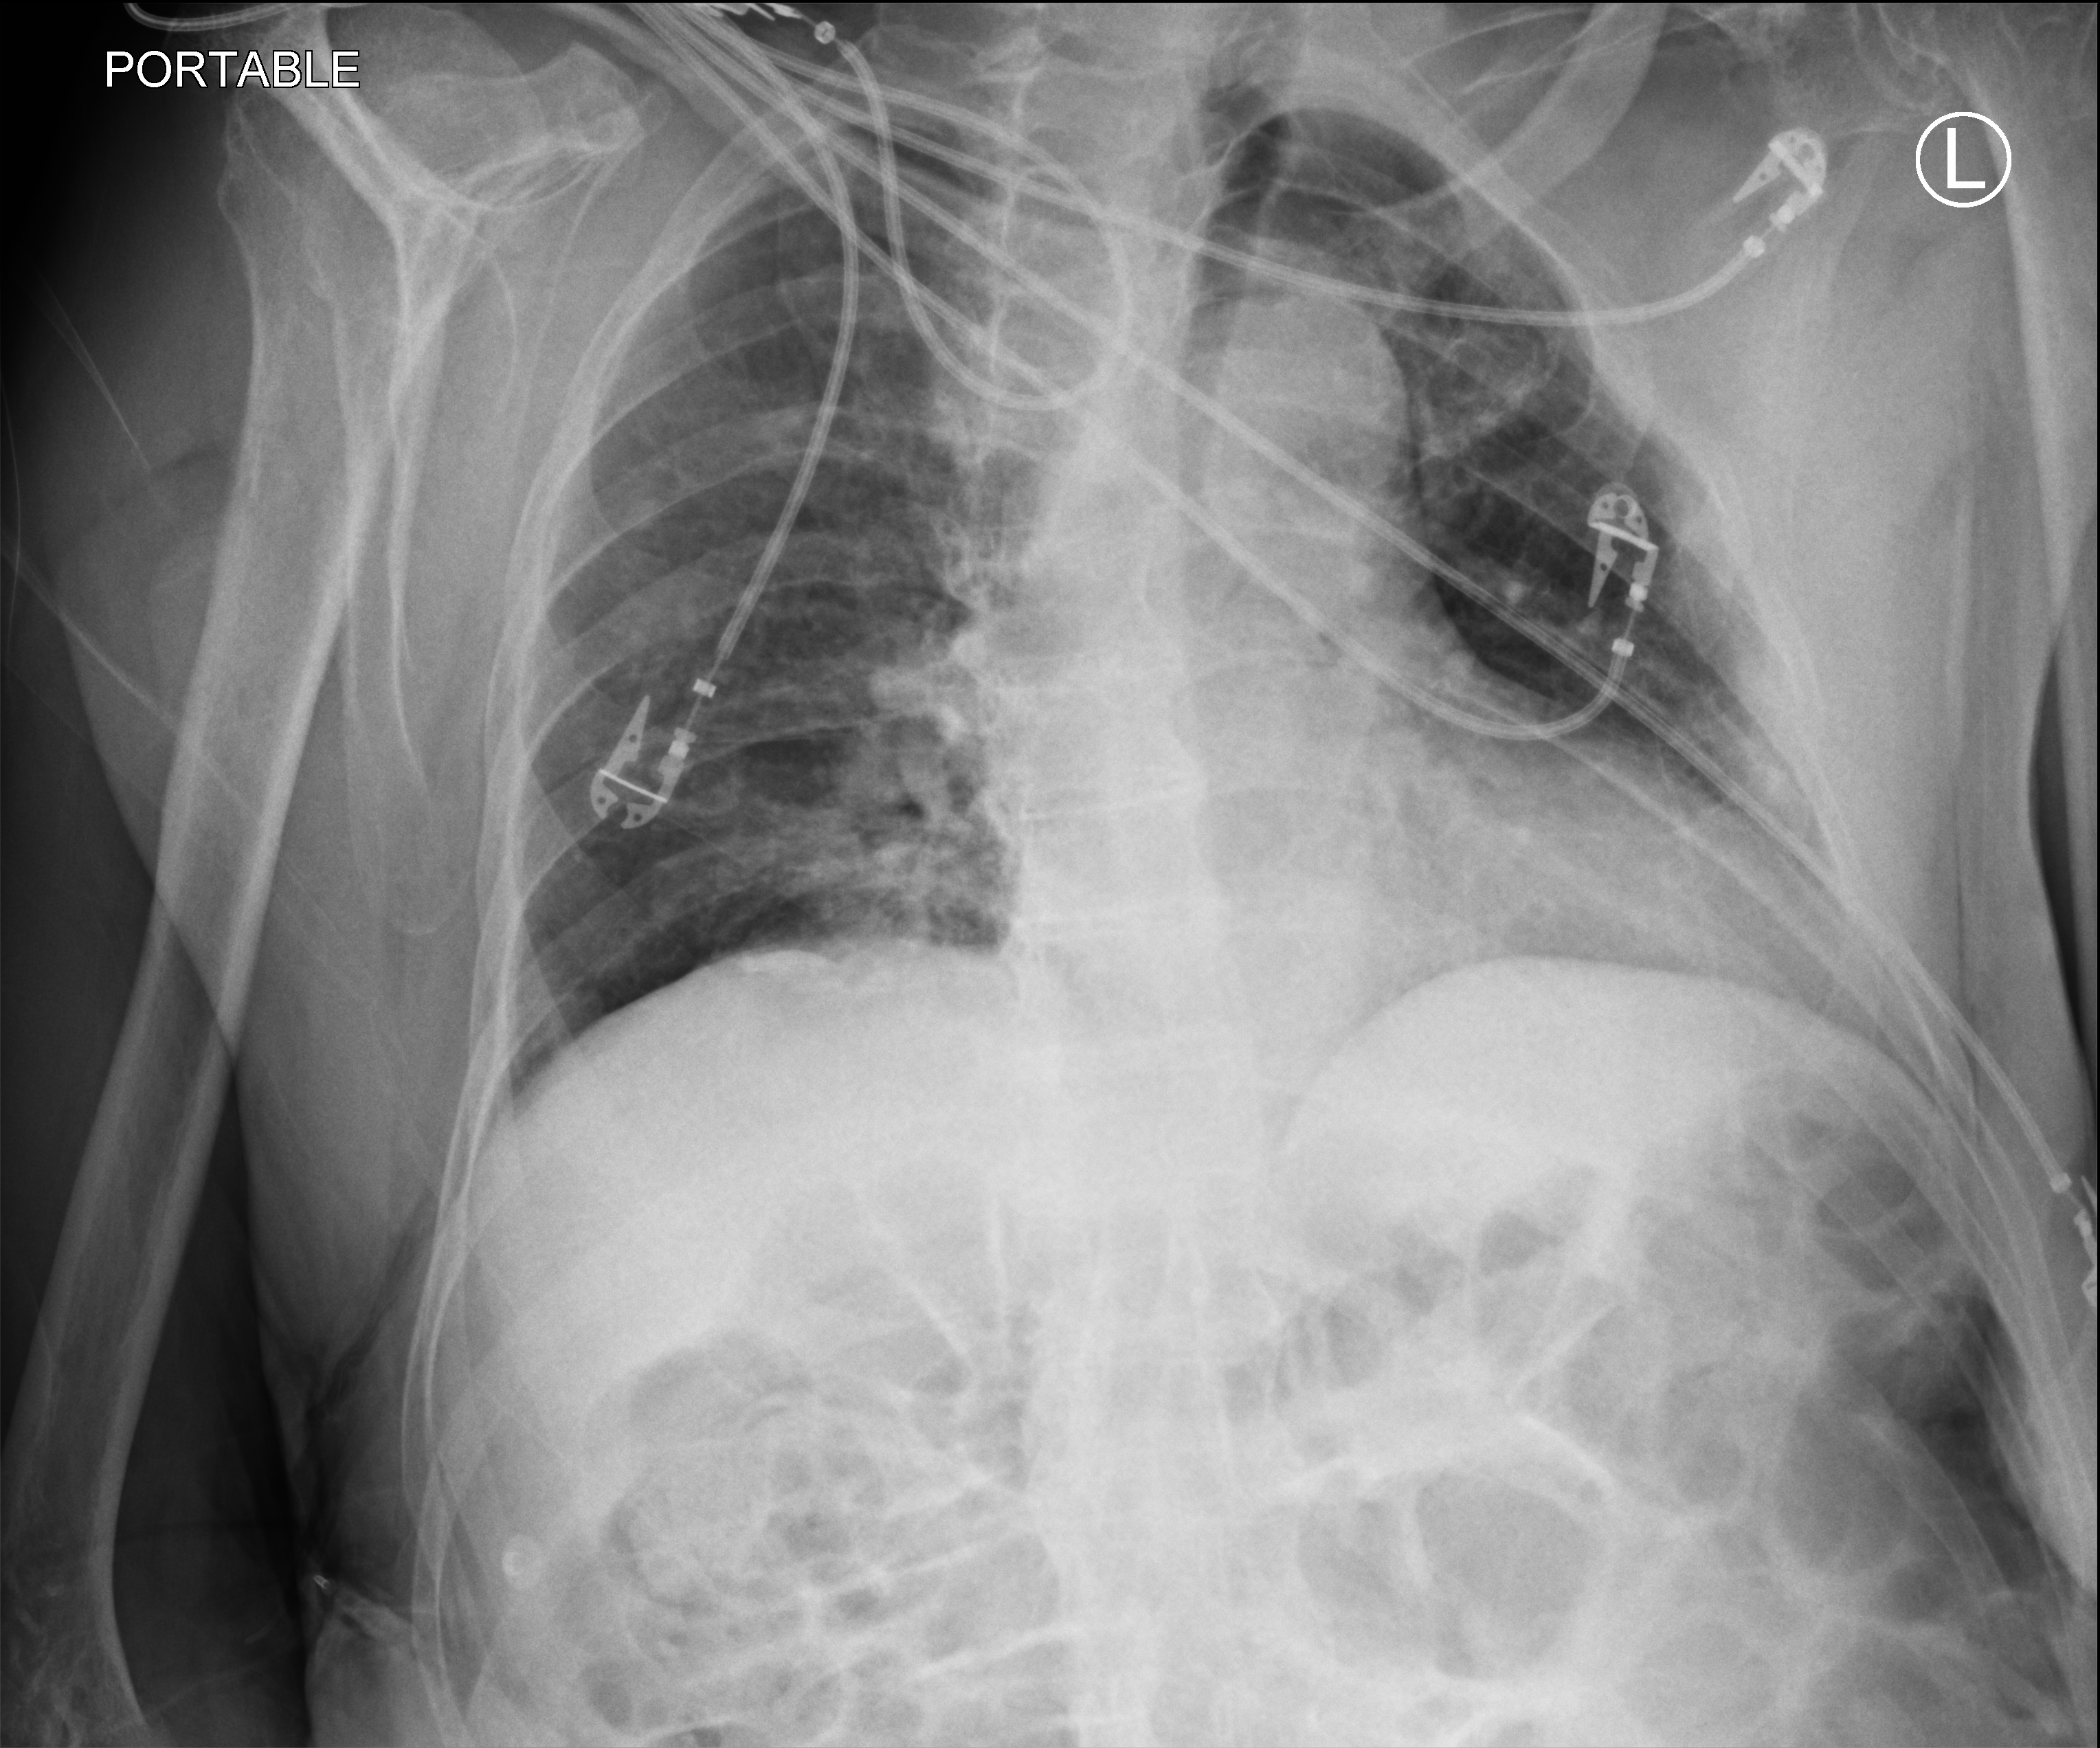
Chest X-ray (portable), anteroposterior (AP) projection. Patient hospitalised with COVID-19; male, aged 75–90 years.
Hospital-stay facts (about this admission, not read from this image; timing relative to this image not recorded): length of hospital stay: 1 day; mechanically ventilated during this hospital stay: no; admitted to intensive care during this hospital stay: no.